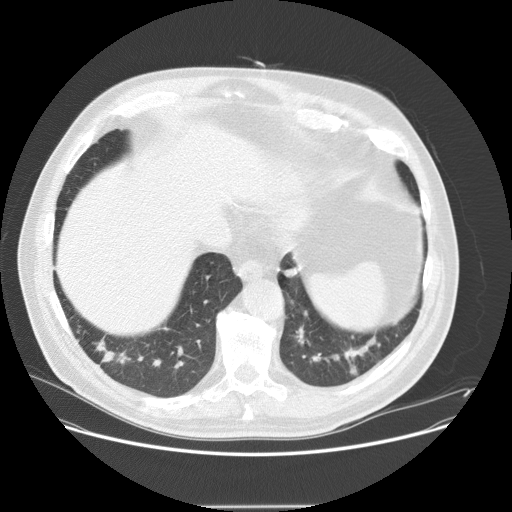
Chest CT (low-dose screening protocol), one axial image; baseline annual screen; lung window (W 1500 / L -600 HU); 2.5 mm slice thickness; 120 kVp; slice 102 of 143 in the series; 512 × 512 image matrix, field of view 400 × 400 mm. Male participant, aged 61 years at enrolment. Current smoker at enrolment.
• Expert reader's lesion annotation, bounding box [x1, y1, x2, y2] px = [89, 332, 142, 383].
• The screening reader recorded 2 non-calcified nodules or masses ≥4 mm on this exam (left lower lobe, right lower lobe); which of them this box marks is not recorded.
• Official screen result: positive, change unspecified: nodule(s) >= 4 mm or enlarging nodule(s), mass(es), or other non-specific abnormalities suspicious for lung cancer.
• Participant outcome: lung cancer diagnosed 41 days after this screen — bronchiolo-alveolar carcinoma, mucinous, right lower lobe, well differentiated (G1), stage IV (AJCC 6th edition), 23 mm at pathology.